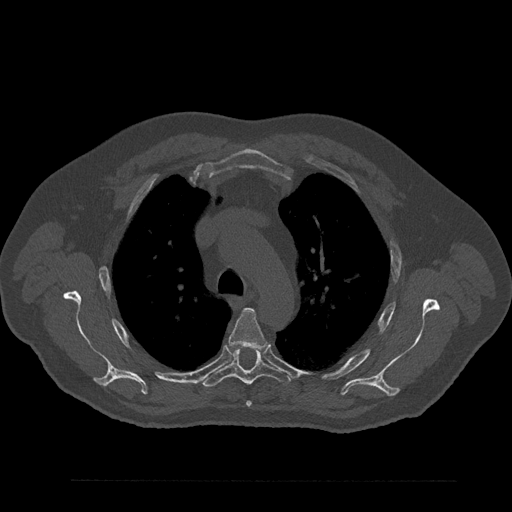
CT including the spine, one axial slice. Position 620 of 797 along the scan axis. Reconstruction kernel Br40s/3. 120 kVp. Bone window (W 1800 / L 400 HU). 0.5 mm slice thickness. 512 × 512 image matrix. Patient: male, 61 years. Case-level facts recorded for this patient, not image findings: primary cancer: prostate.
Structures marked on this image (semi-automatically segmented with operator editing):
- T4 vertebra: bounding box <228,308,266,407> (left, top, right, bottom; pixels)
- T5 vertebra: <201,349,290,387>